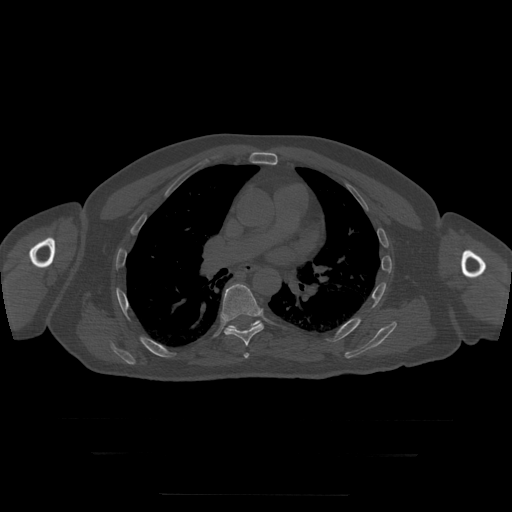
CT including the spine, one axial slice. Position 184 of 397 along the scan axis. Reconstruction kernel STANDARD. 120 kVp. Bone window (W 1800 / L 400 HU). 512 × 512 image matrix, field of view 510 × 510 mm. Patient age 73 years. Case-level facts recorded for this patient, not image findings: primary cancer: prostate.
Annotated regions visible in this slice (semi-automatic segmentation, software-assisted and operator-edited):
- T6 vertebra: bounding box <244,353,249,359> (left, top, right, bottom; pixels)
- T7 vertebra: <222,284,264,346>
- T8 vertebra: <227,320,261,330>